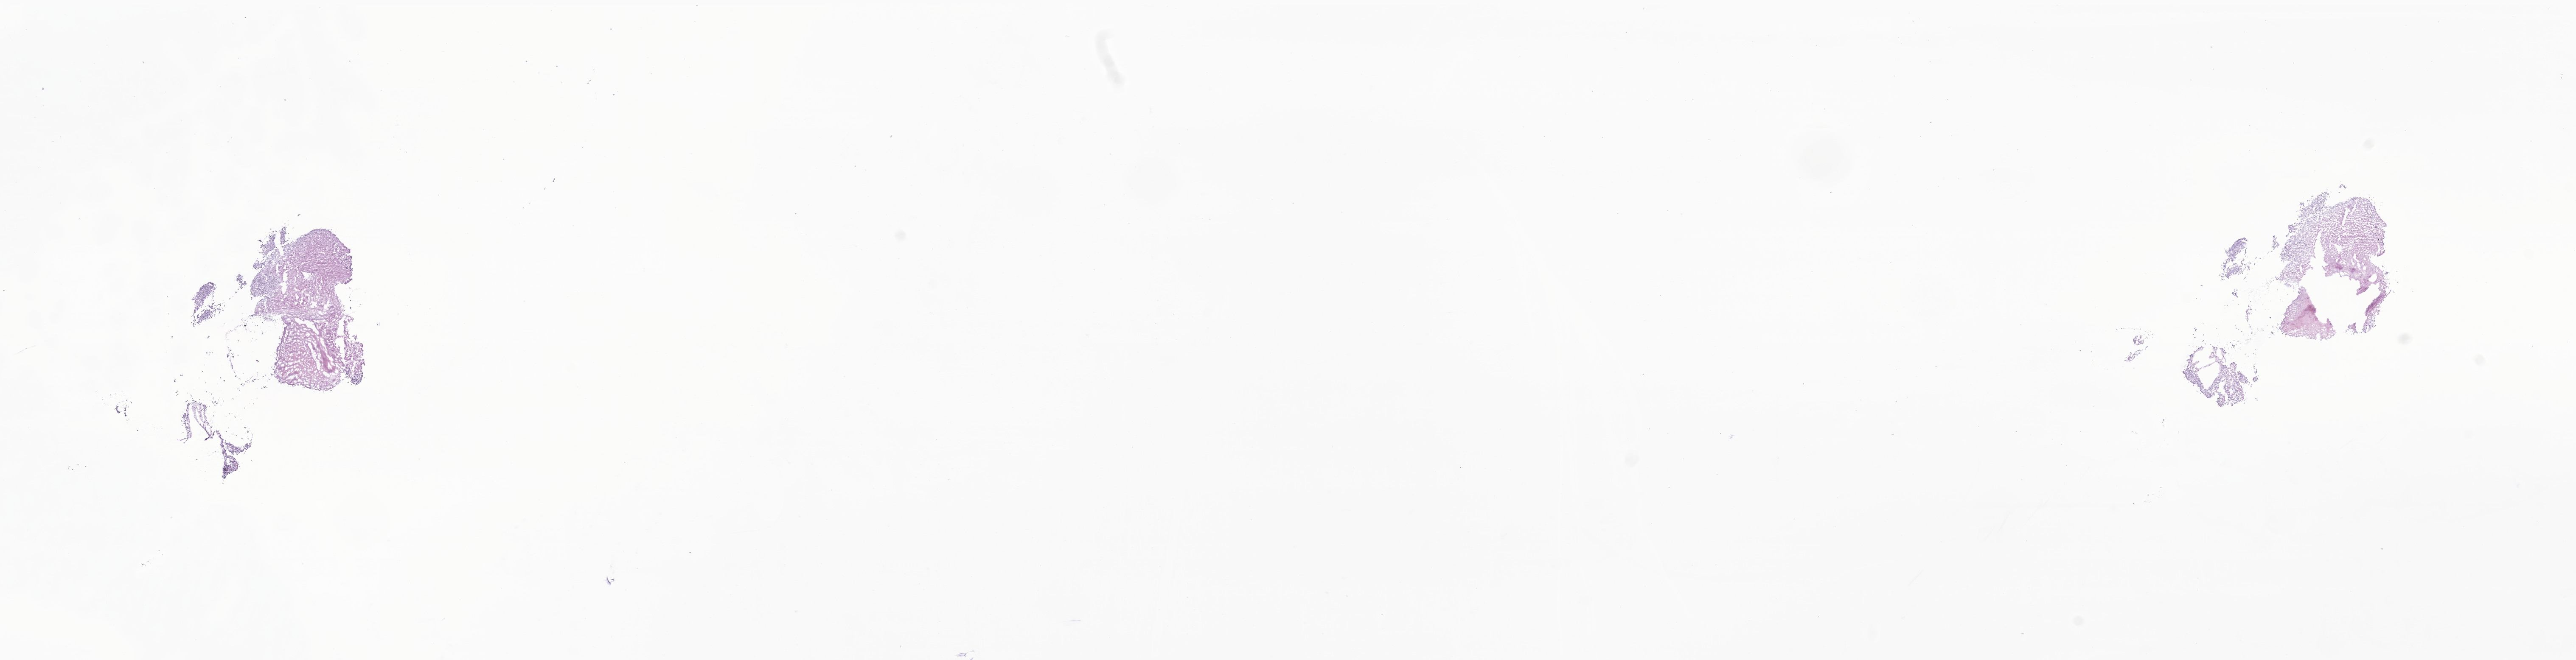
Digitized haematoxylin and eosin-stained section of tumor tissue from the long bone of lower limb — shown as a low-resolution overview of the whole scanned area (about 25.6 x 6.6 mm). Frozen section. Patient: male, age 170 months (14 years 2 months).
* tissue or organ of origin (case record): long bones of lower limb and associated joints
* diagnosis (ICD-O-3 morphology term): Spindle cell sarcoma